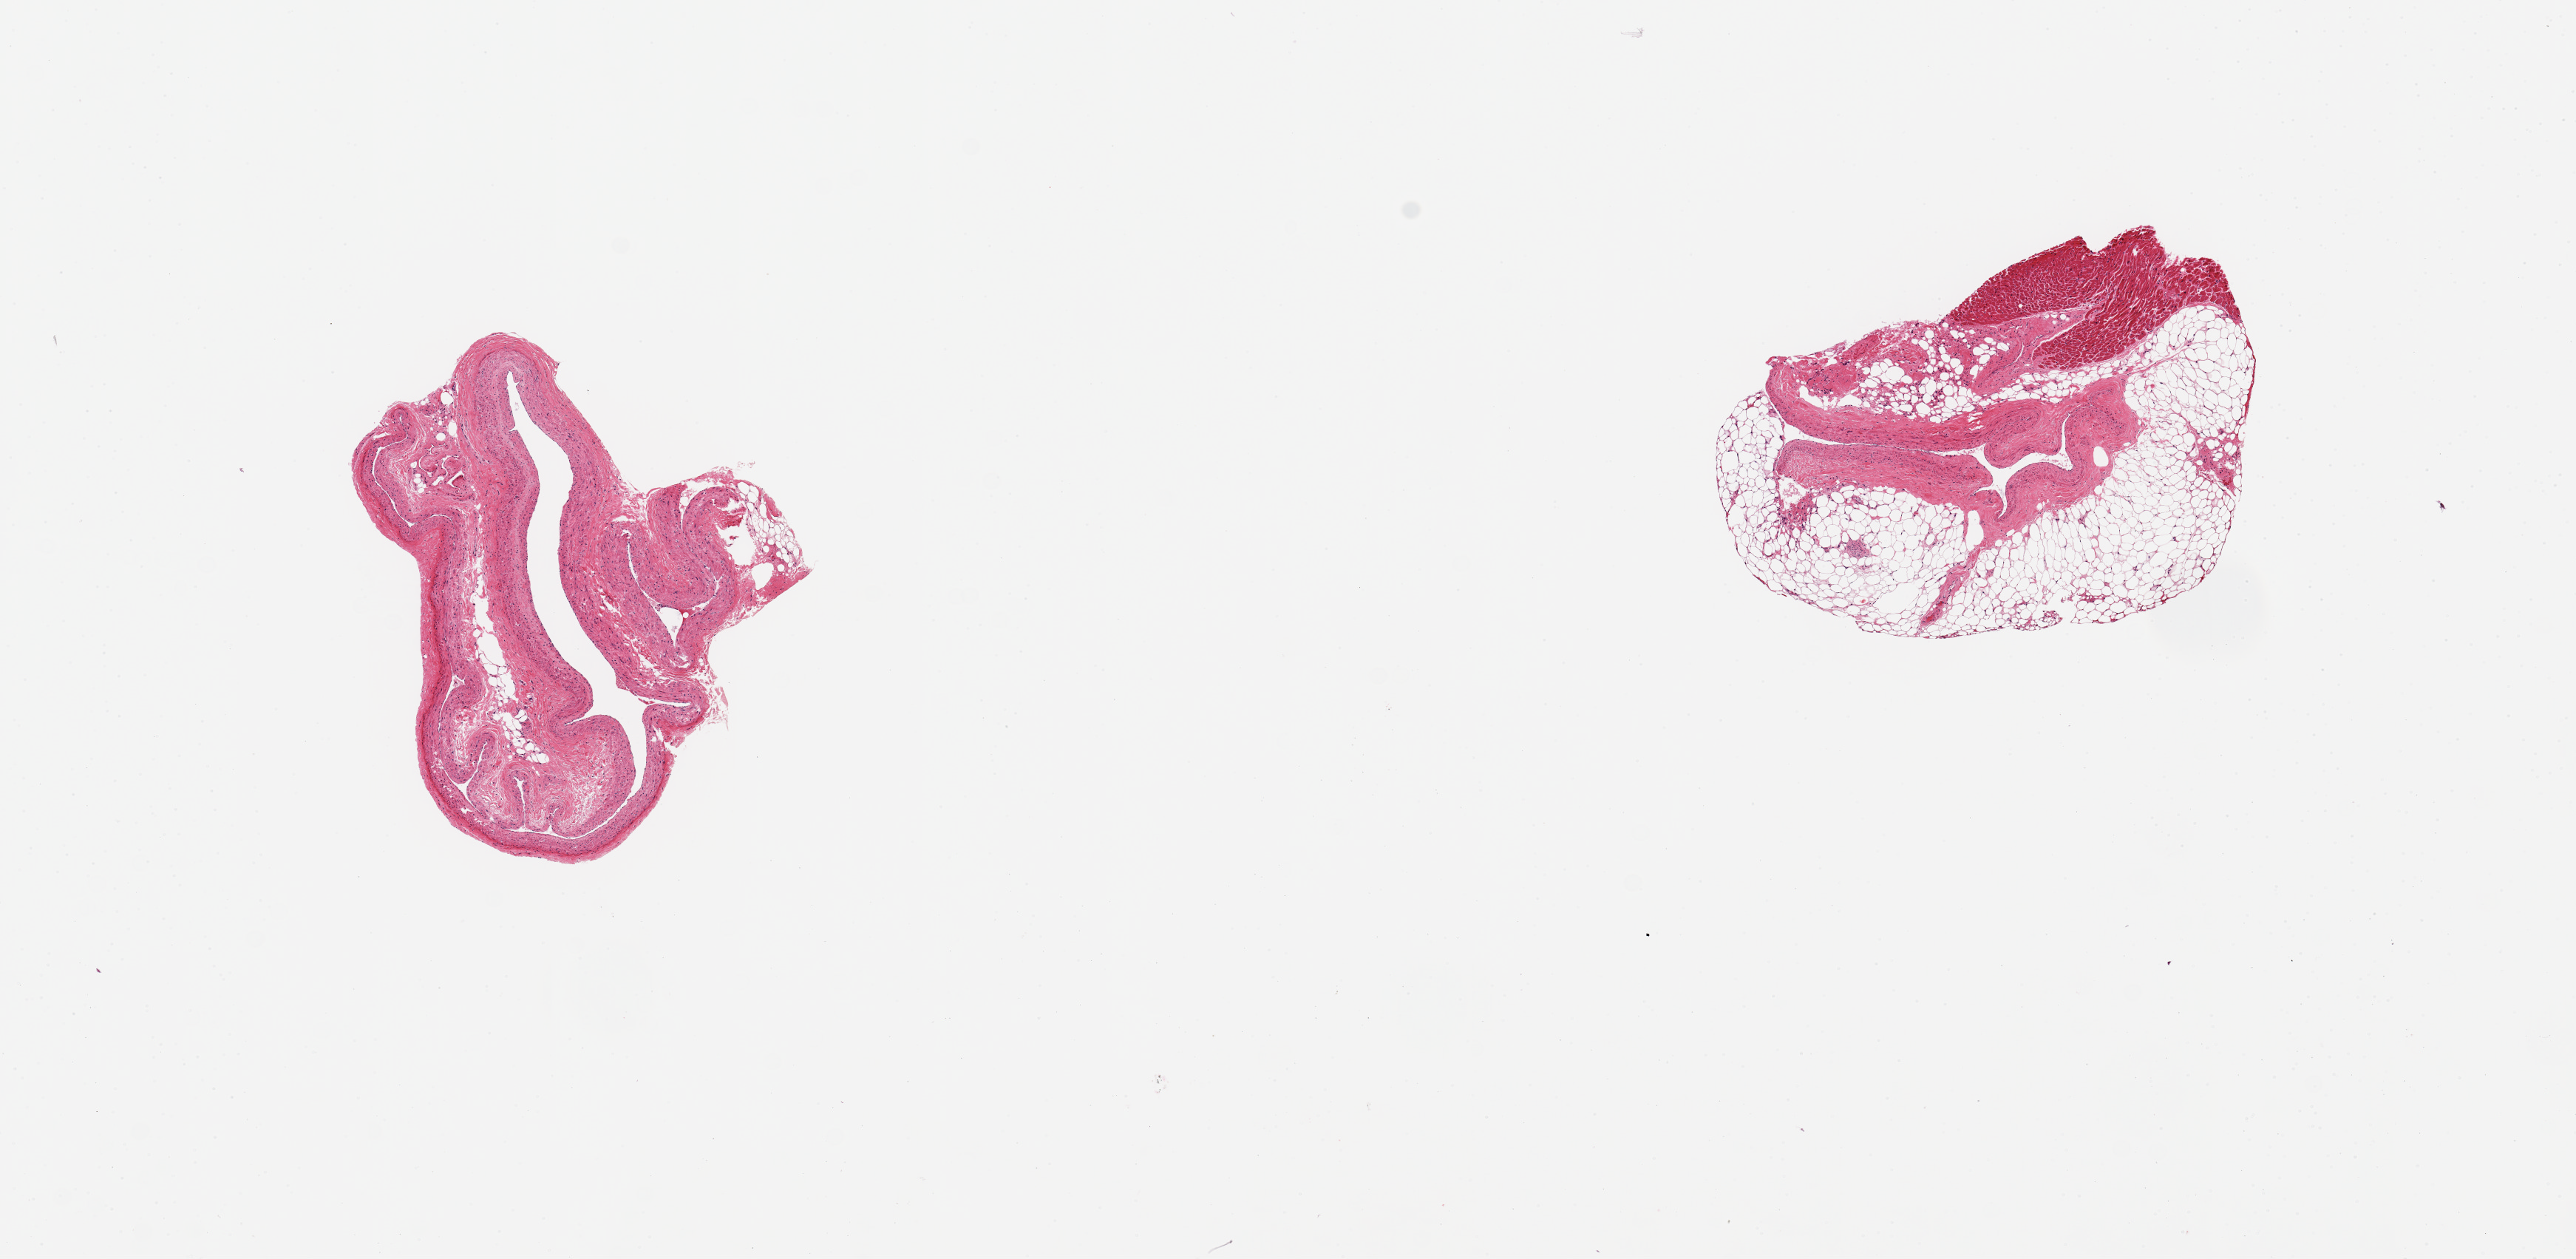
Whole-slide image, haematoxylin and eosin stain, a low-resolution overview of the entire scanned area, about 13.8 x 6.7 mm (acquisition: 20x scan). PAXgene-fixed, paraffin-embedded tissue. Target tissue: coronary artery. Tissue donor sample.
- review note (as recorded): 2 pieces, ~2.5 mm each; 1 has ~60% adipose and 20% myocardium